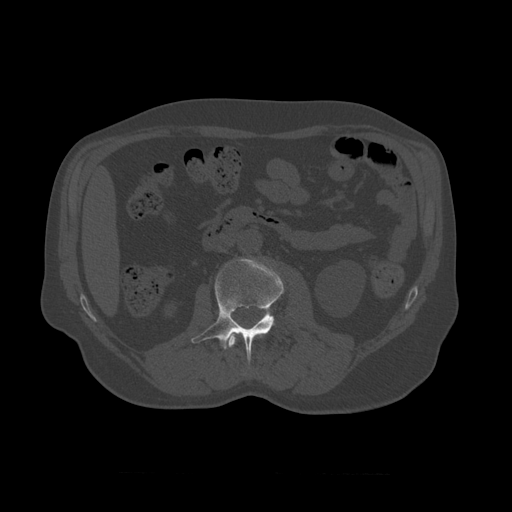
CT including the spine, one axial slice. Slice 329 of 450 in the series (ordered by position). 120 kVp. Bone window (W 1800 / L 400 HU). 1.25 mm slice thickness. 512 × 512 image matrix, field of view 405 × 405 mm. Patient age 75 years. From the clinical record (not read from this slice): primary cancer: prostate.
Annotated regions visible in this slice (semi-automatic segmentation, software-assisted and operator-edited):
- L1 vertebra: bounding box (x1, y1, x2, y2) in pixels: (227, 334, 261, 348)
- L2 vertebra: (191, 258, 285, 365)